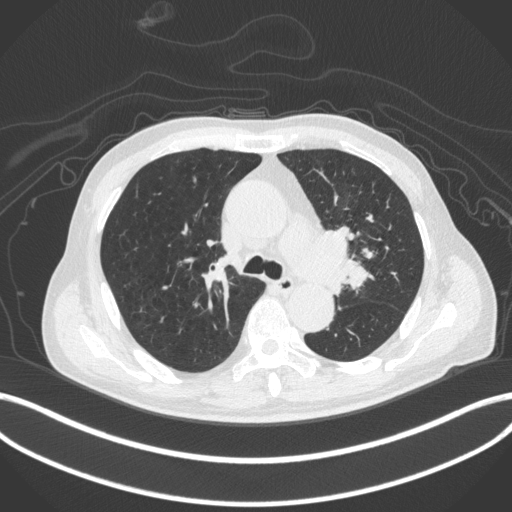
Chest CT, one axial slice; position 287 of 420 along the scan axis; reconstruction kernel B31f; lung window (W 1500 / L -600 HU); 512 × 512 image matrix, field of view 400 × 400 mm. Male patient, age 77 years. Case-level facts recorded for this patient, not image findings: clinical TNM (as recorded): T3 N1 M0.
Outlined on this slice (rectangle marked by the reading radiologist):
- lung tumour (recorded histology: adenocarcinoma): box from (x=310, y=220) to (x=367, y=298) px